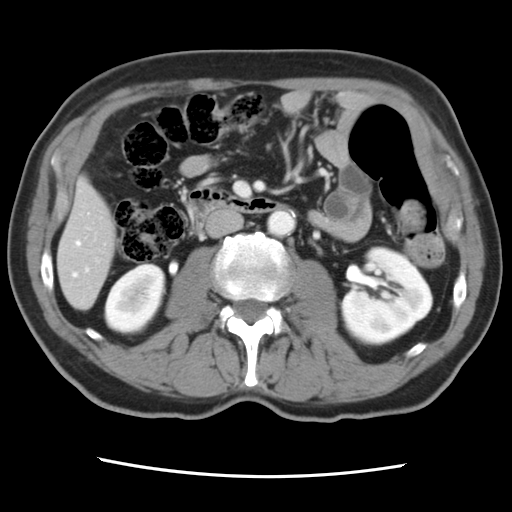
Contrast-enhanced abdominal CT, one axial slice. Slice 25 of 83 in the series (ordered by position). 120 kVp. Soft-tissue window (W 400 / L 40 HU). 5 mm slice thickness. 512 × 512 image matrix, field of view 321 × 321 mm. Male patient, age 69 years. From the clinical record (not read from this slice): diagnosis: colorectal cancer liver metastases, imaged before liver resection; multiple liver metastases: yes; largest metastasis: 3.5 cm; disease in both lobes: no.
Outlined on this slice (outlined manually by an expert reader):
- hepatic veins: box from (x=73, y=241) to (x=81, y=277) px
- liver: (x=59, y=183)–(x=114, y=309)
- planned liver remnant (the part of the liver to remain after resection): (x=59, y=183)–(x=115, y=308)
- portal vein (with intrahepatic branches): (x=86, y=268)–(x=89, y=271)